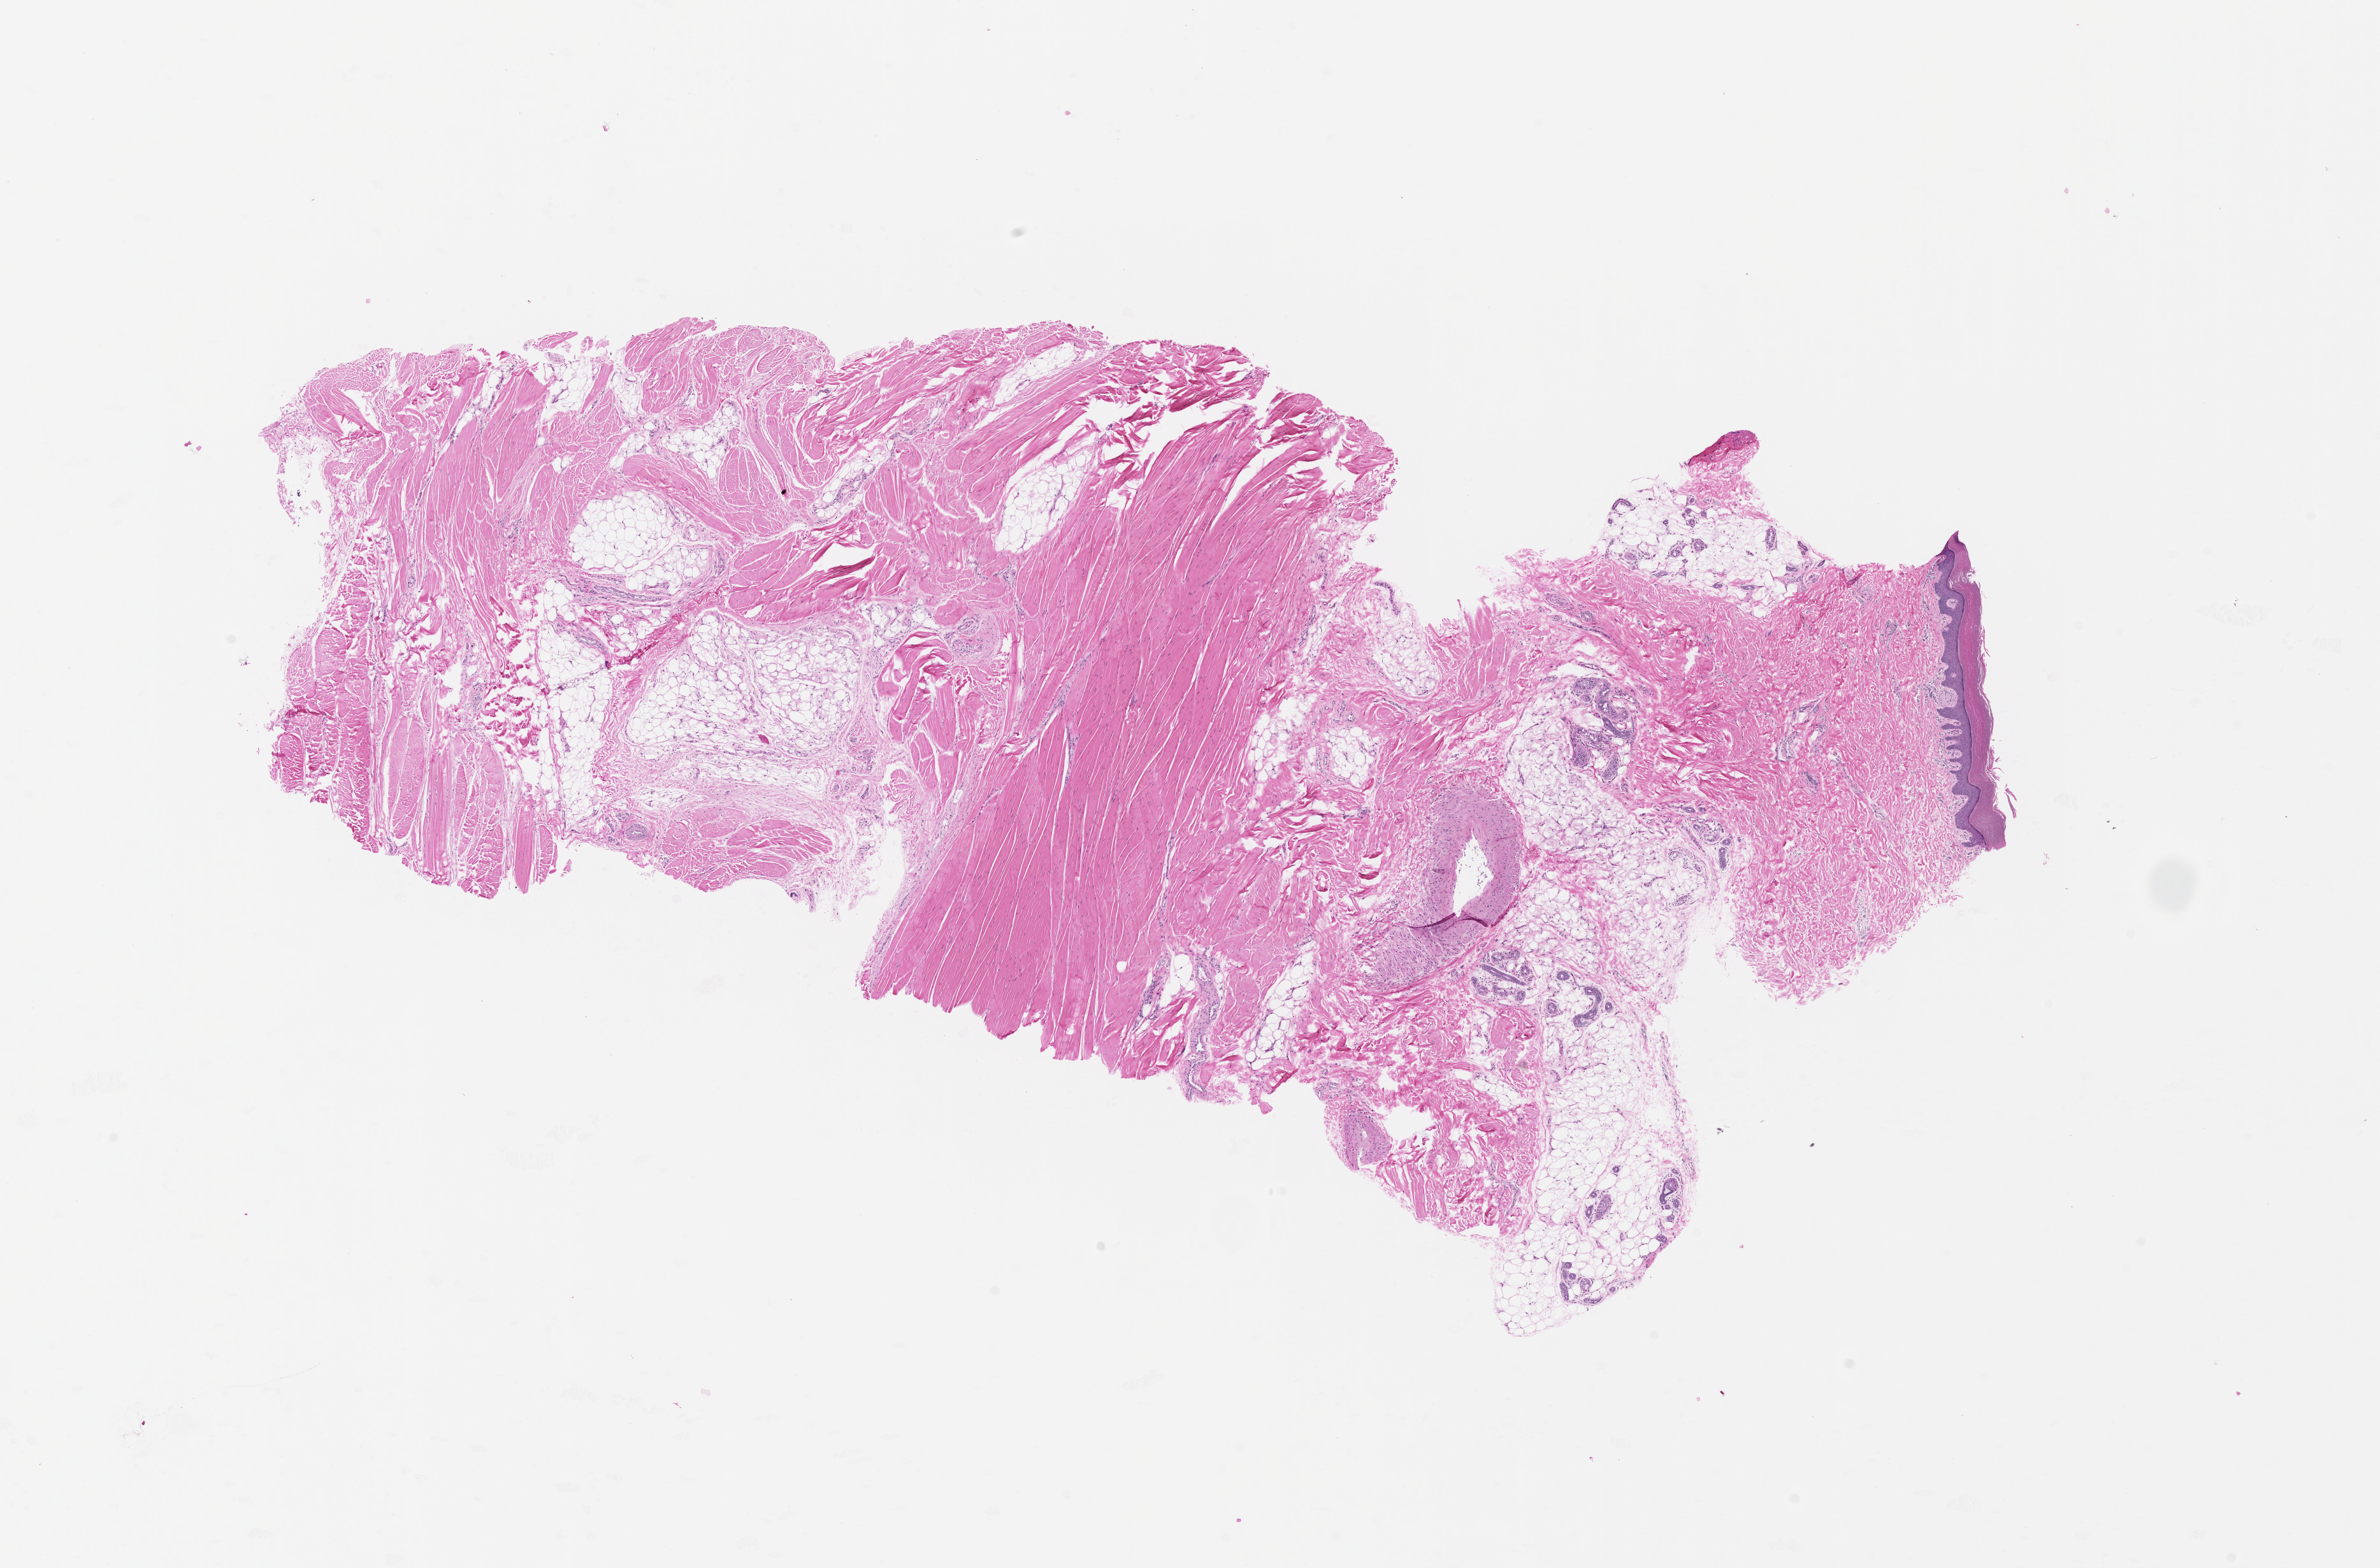
Digitized H&E-stained tissue section (whole slide) — shown as a low-resolution overview of the whole scanned area (about 15.0 x 9.9 mm, from a 20x scan). 64-year-old male patient.
- patient diagnosis: Malignant melanoma, NOS